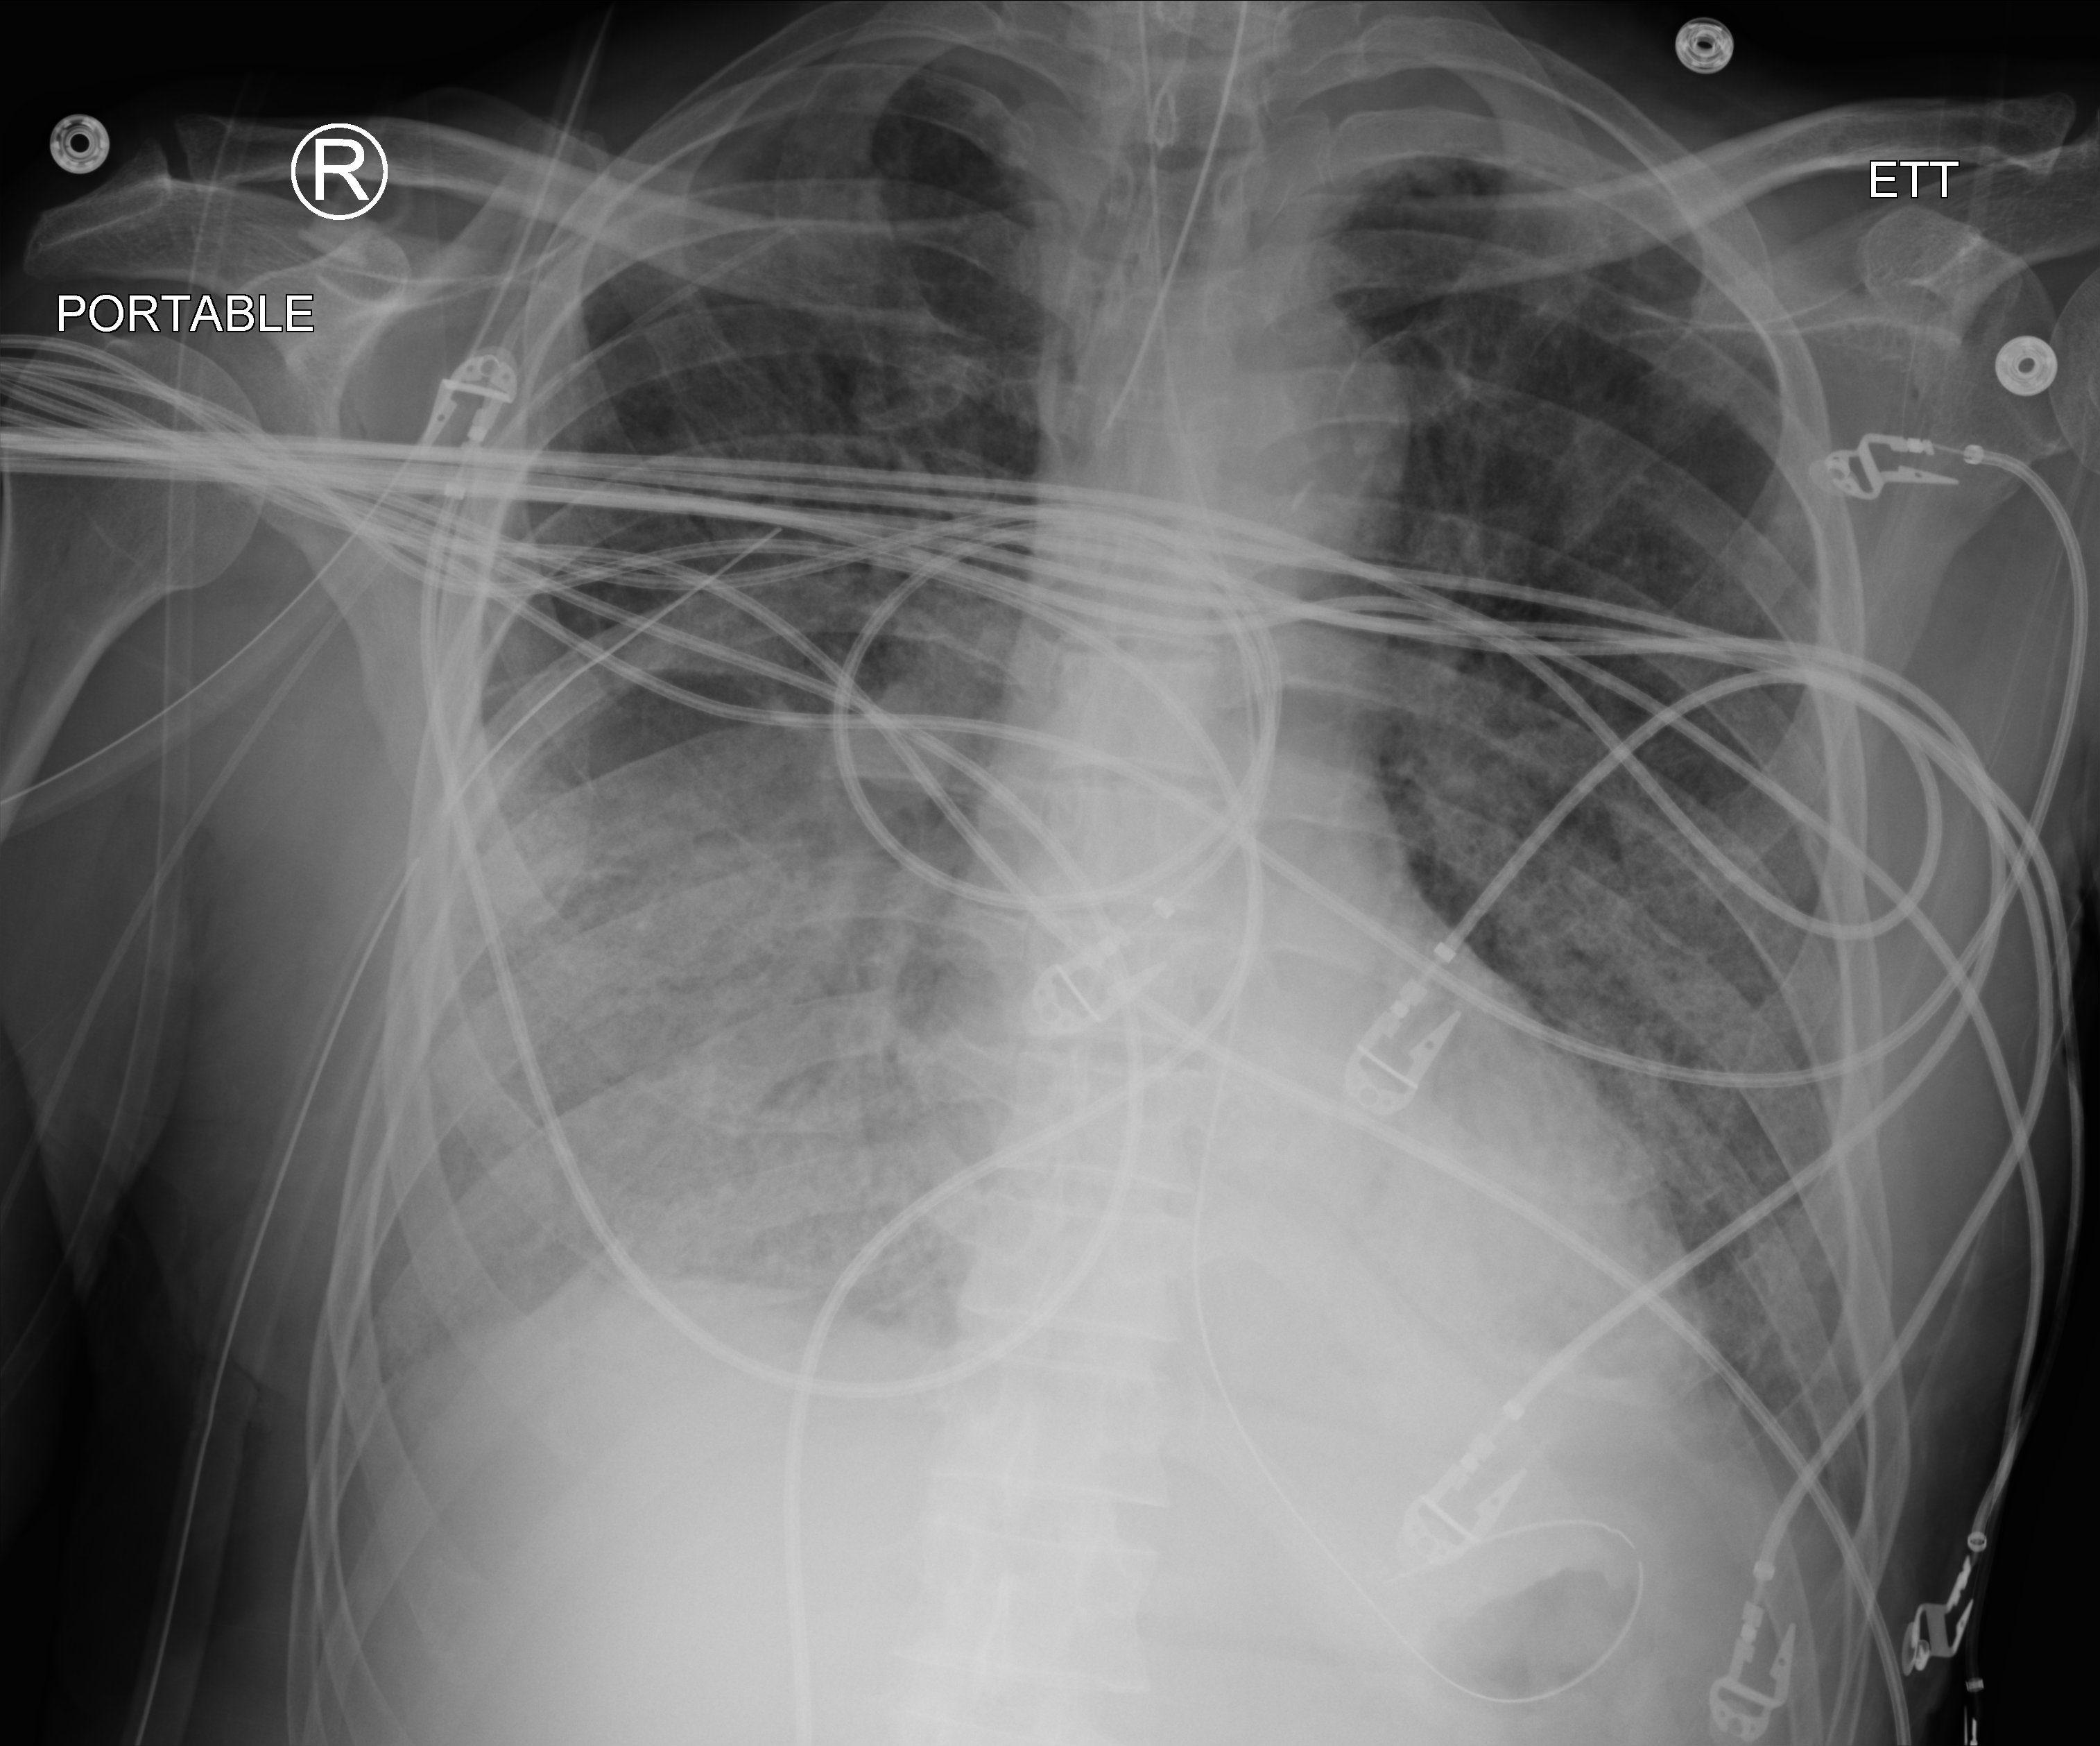
Bedside chest radiograph (computed radiography), anteroposterior (AP) projection. Male patient hospitalised with COVID-19, age 60–74 years.
Admission-level facts for this patient (not findings on this image; timing relative to this image not recorded): length of hospital stay: 31 days; mechanically ventilated during this hospital stay: yes; admitted to intensive care during this hospital stay: yes.